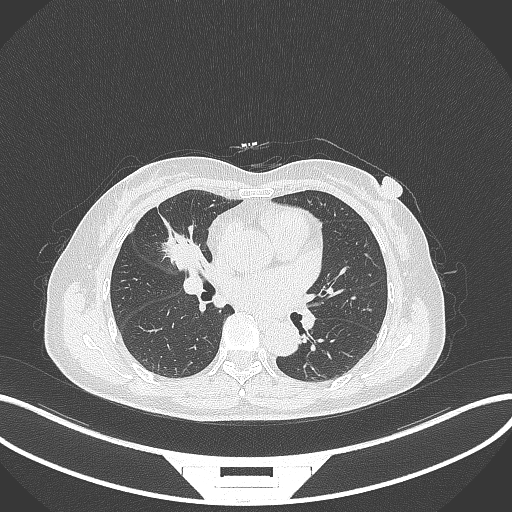
Chest CT, one axial slice; slice 155 of 284 in the series (ordered by position); reconstruction kernel B70f; 120 kVp; lung window (W 1500 / L -600 HU); 1 mm slice thickness; 512 × 512 image matrix, field of view 400 × 400 mm. Patient: female, 51 years. Case-level facts recorded for this patient, not image findings: clinical TNM (as recorded): T1c N0 M0; histopathological grade: G2.
Annotated regions visible in this slice (rectangle marked by the reading radiologist):
- lung tumour (recorded histology: adenocarcinoma): bounding box <162,223,203,272> (left, top, right, bottom; pixels)